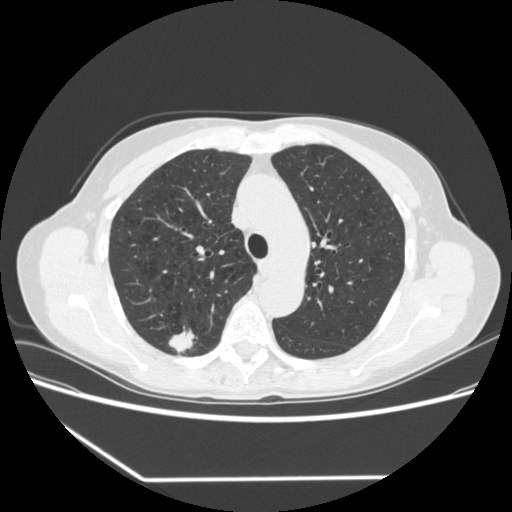
Low-dose screening chest CT, one axial slice; slice 241 of 323 in the series (ordered by position); lung window (W 1500 / L -600 HU); 512 × 512 image matrix.
Annotated regions visible in this slice (outlined manually by an expert reader):
- lesion 1 (tumor, upper lobe of right lung): bounding box <168,326,198,354> (left, top, right, bottom; pixels)